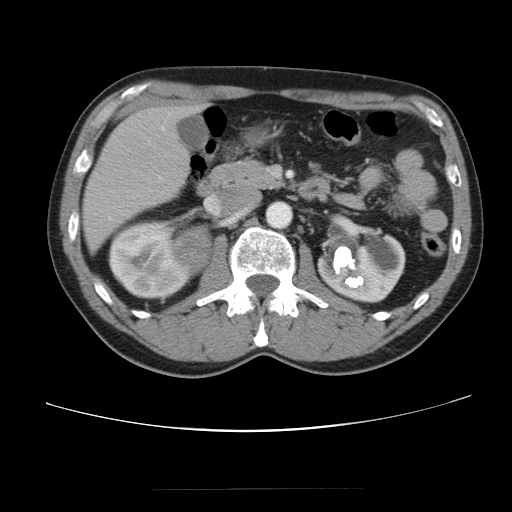
Contrast-enhanced abdominal CT, one axial slice; position 57 of 80 along the scan axis; intravenous contrast given; soft-tissue window (W 400 / L 40 HU); 512 × 512 image matrix. Patient: male, 61 years. Case-level facts recorded for this patient, not image findings: diagnosis: adrenocortical carcinoma; tumour side: right adrenal; tumour size at pathology: 11.1 cm; Ki-67 index: 32 %; stage (as recorded): 2.
Outlined on this slice (semi-automatic segmentation, software-assisted and operator-edited):
- mass: box from (x=174, y=224) to (x=212, y=272) px